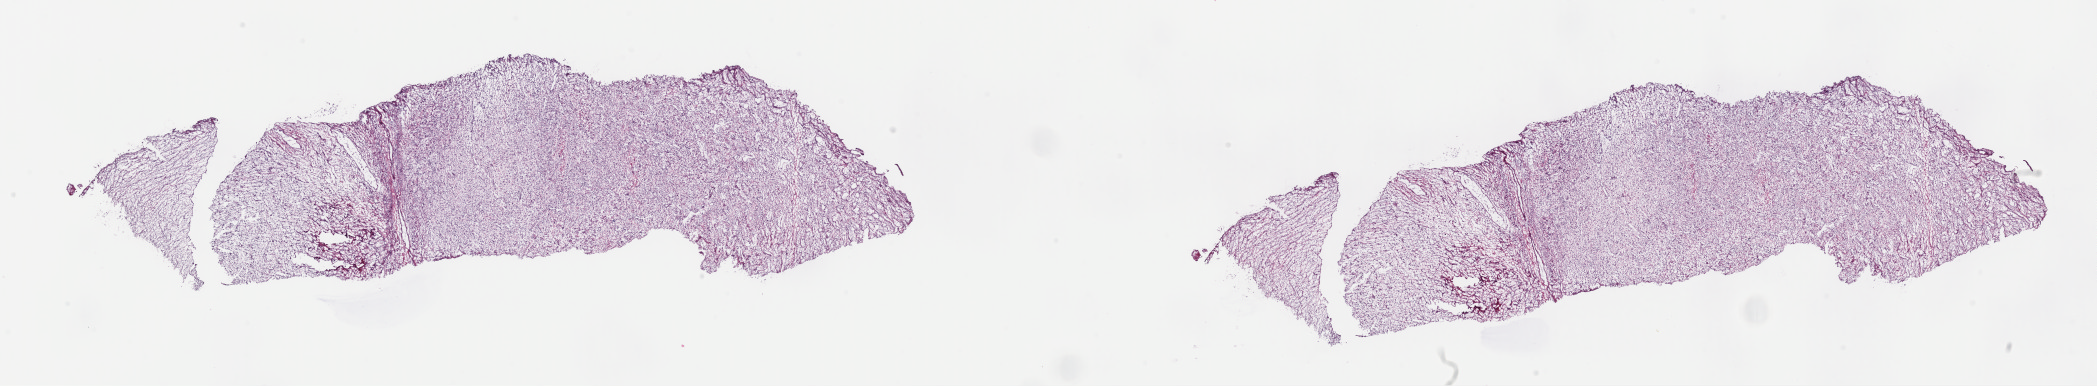
Digitized H&E tissue section (whole slide), shown as a low-resolution overview of the whole scanned area (about 33.1 x 6.1 mm, acquisition: 40x scan). Frozen section from the top of the tissue portion. Retroperitoneum and peritoneum, primary tumour sample. Patient: male, age at initial diagnosis 43 years. Pathologist review of this section (percent, as recorded): tumour cells 99%, tumour nuclei 95%, normal cells 0%, stromal cells 1%, necrosis 0%. Infiltration values recorded for this section: lymphocyte infiltration 0%, monocyte infiltration 0%, neutrophil infiltration 0%.
Diagnosis: Dedifferentiated liposarcoma (retroperitoneum).